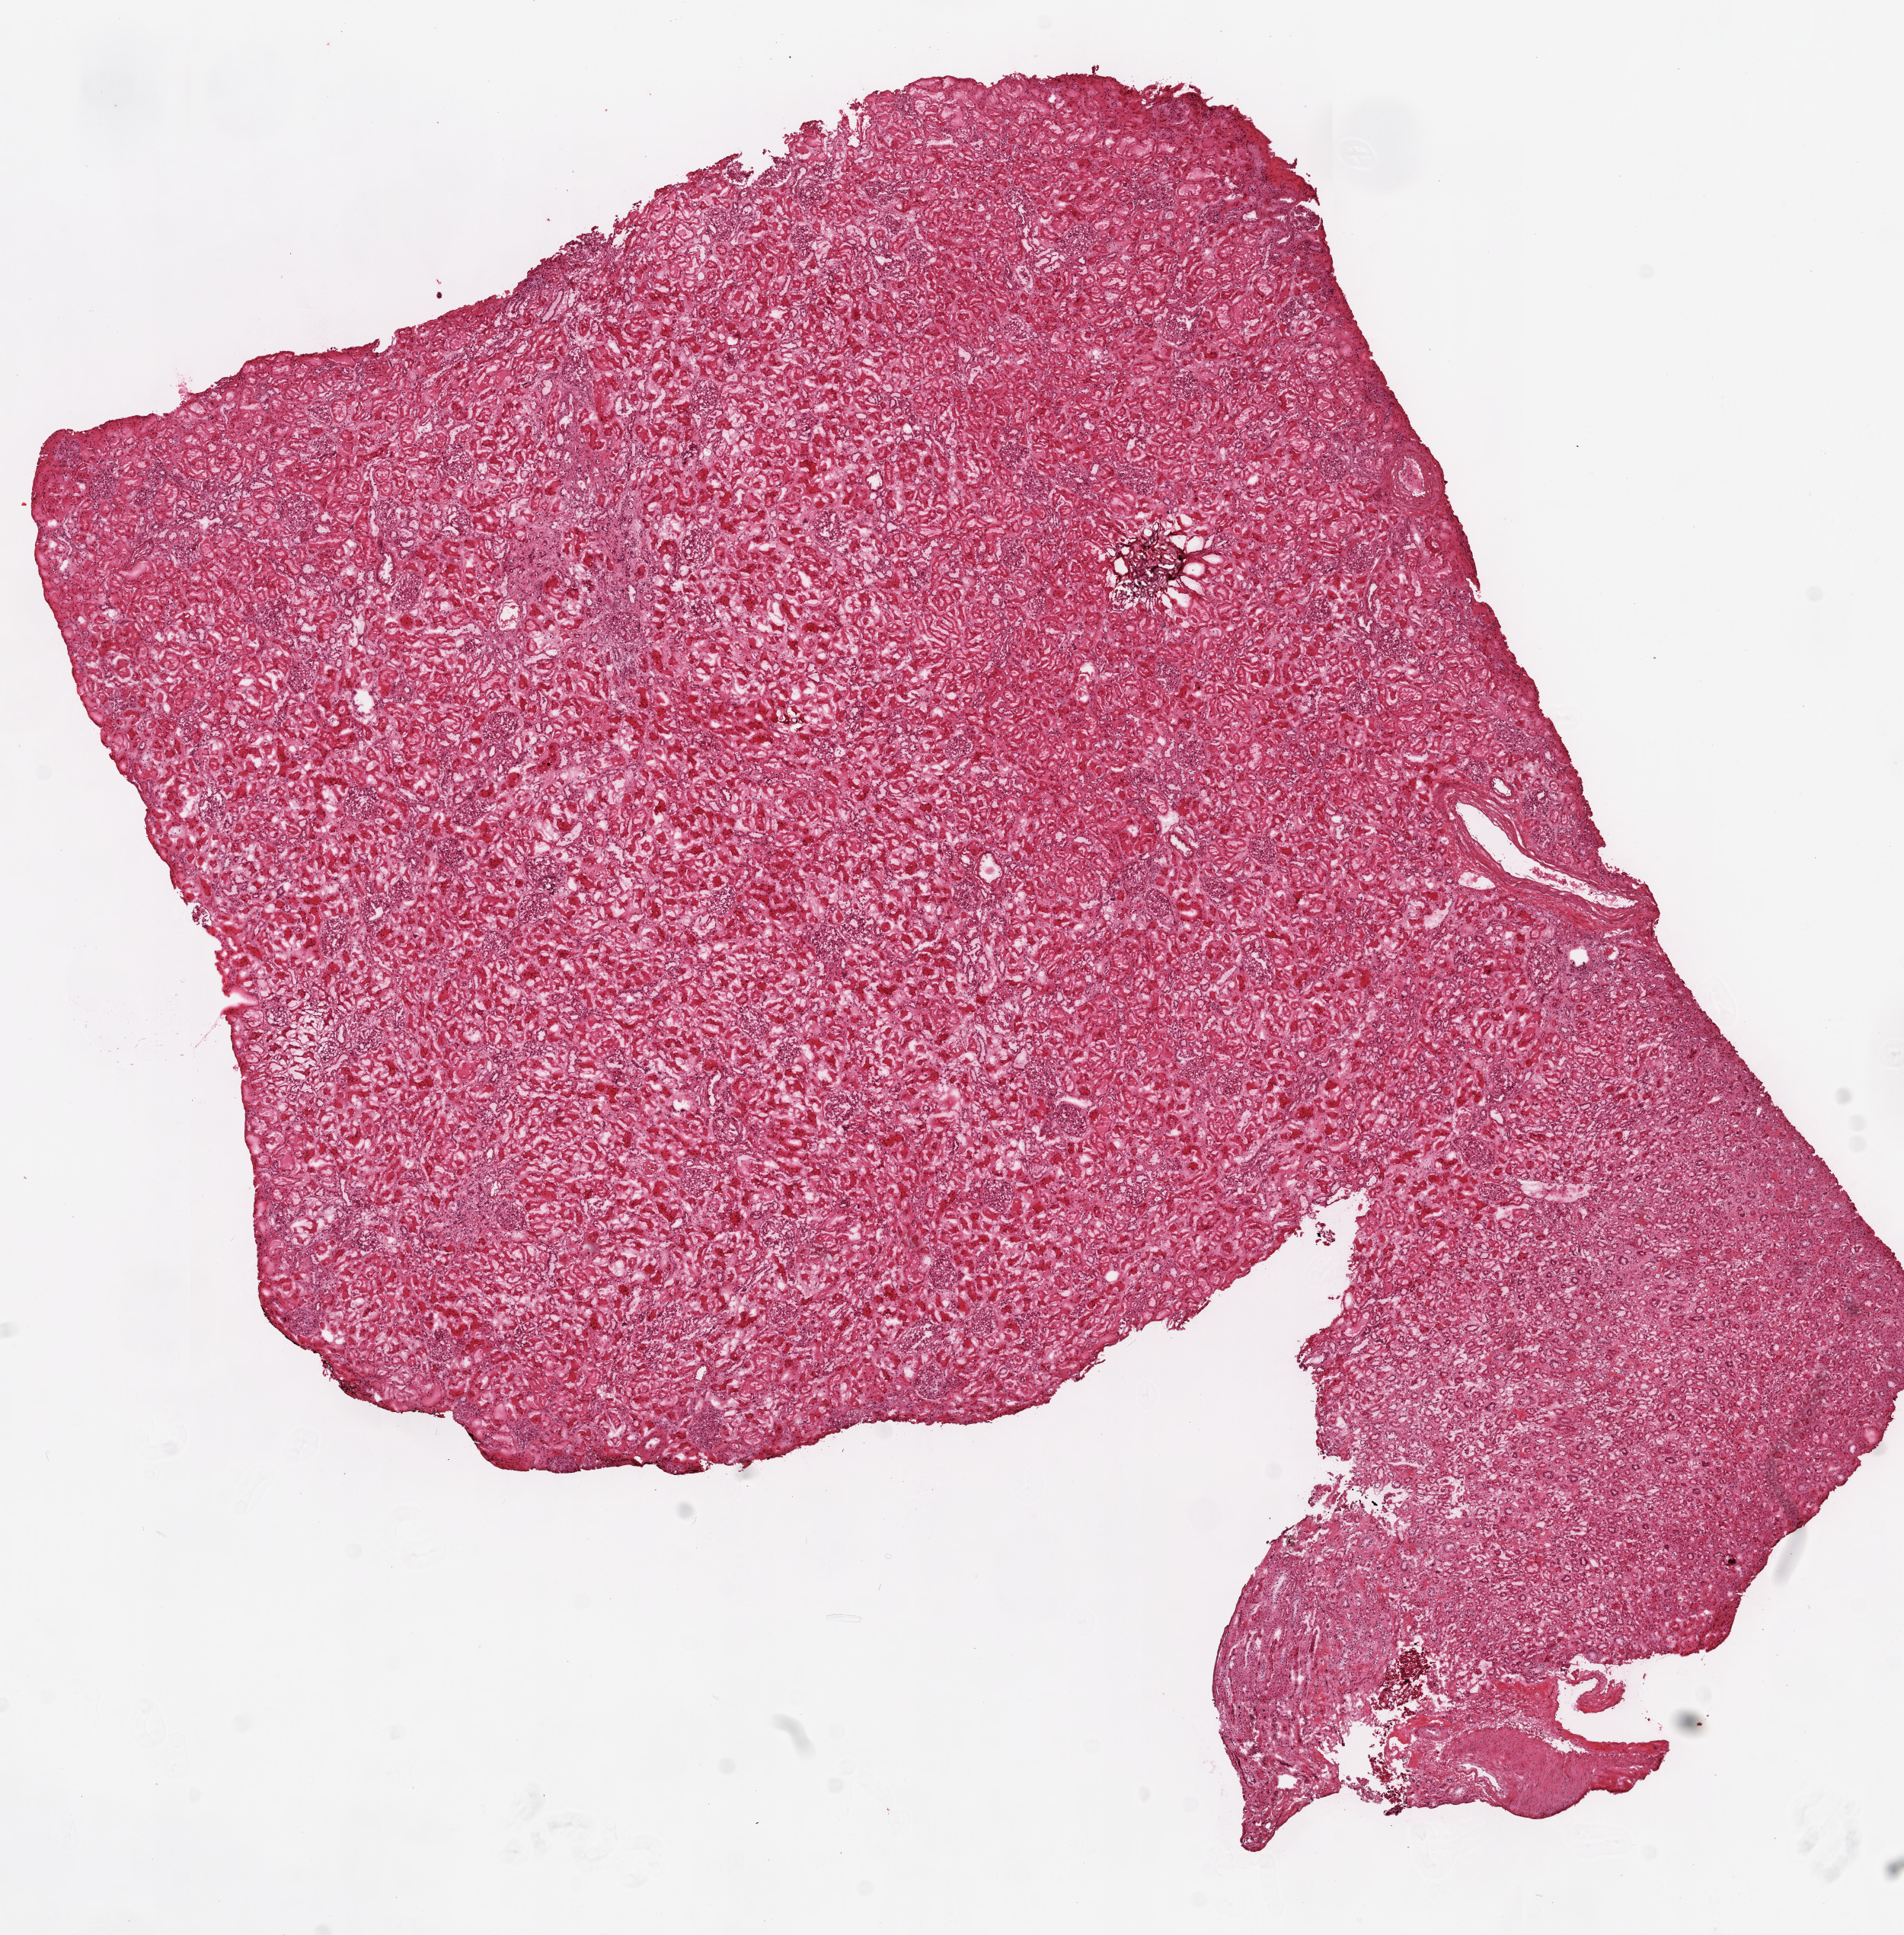
Digitized Hematoxylin and eosin (H&E) stained tissue section (whole slide), shown as a low-resolution overview of the whole scanned area (about 10.0 x 10.2 mm, slide scanned at 20x), frozen section, kidney, solid tissue normal (non-tumour tissue) sample. Male, age 61 years at initial diagnosis.
This section: solid tissue normal sample (biorepository sample class). Patient diagnosis: Clear cell adenocarcinoma, NOS.